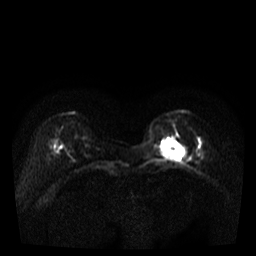
Breast MRI, one axial slice. Position 10 of 35 along the scan axis. Diffusion-weighted series; image 2 of 4 stored at this slice position (different b-values; order by instance number). 3 T. 5 mm slice thickness. 256 × 256 image matrix, field of view 320 × 320 mm. Female patient.
Annotated regions visible in this slice (manually delineated by an expert):
- tumour on diffusion-weighted imaging: box from (x=162, y=139) to (x=184, y=160) px